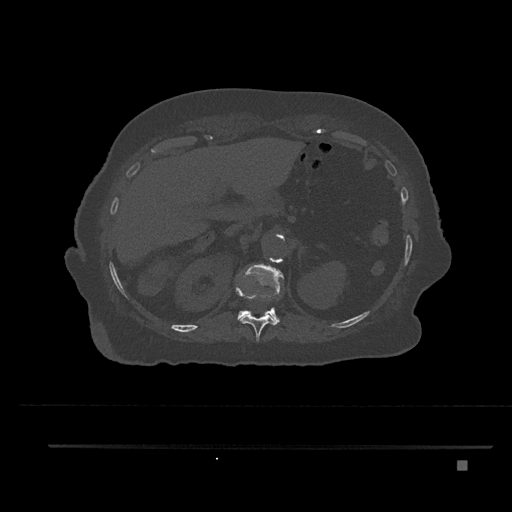
CT including the spine, one axial slice. Position 293 of 797 along the scan axis. Reconstruction kernel Br40s/3. Bone window (W 1800 / L 400 HU). 512 × 512 image matrix, field of view 437 × 437 mm. Female patient, age 76 years. Case-level facts recorded for this patient, not image findings: primary cancer: lung; vertebrae with lytic lesions (as recorded): T11, L3.
Outlined on this slice (semi-automatic segmentation, software-assisted and operator-edited):
- T11 vertebra: bounding box <235,286,278,341> (left, top, right, bottom; pixels)
- T12 vertebra: <235,265,283,323>